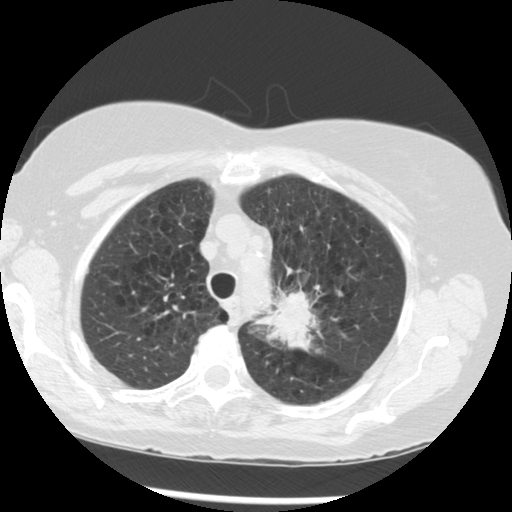
Low-dose screening chest CT, one axial slice. Position 222 of 283 along the scan axis. Reconstruction kernel STANDARD. 120 kVp. Lung window (W 1500 / L -600 HU). 512 × 512 image matrix, field of view 330 × 330 mm.
Structures marked on this image (expert manual segmentation):
- lesion 1 (tumor, upper lobe of left lung): bounding box [x1, y1, x2, y2] px = [254, 291, 321, 351]